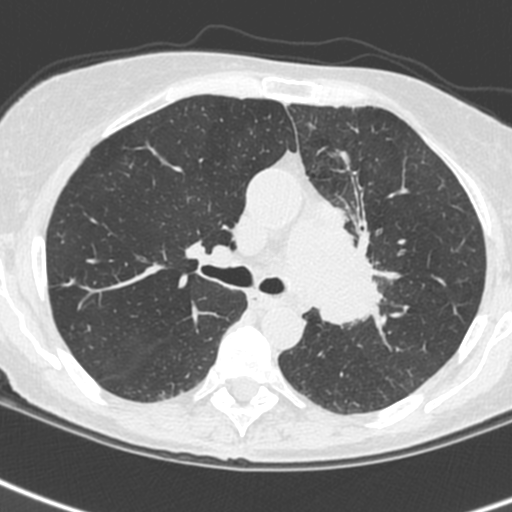
Low-dose screening chest CT, one axial slice; position 158 of 242 along the scan axis; lung window (W 1500 / L -600 HU); 512 × 512 image matrix, field of view 284 × 284 mm.
Outlined on this slice (expert manual segmentation):
- lesion 3 (tumor, upper lobe of left lung): bounding box (x1, y1, x2, y2) in pixels: (316, 199, 381, 326)